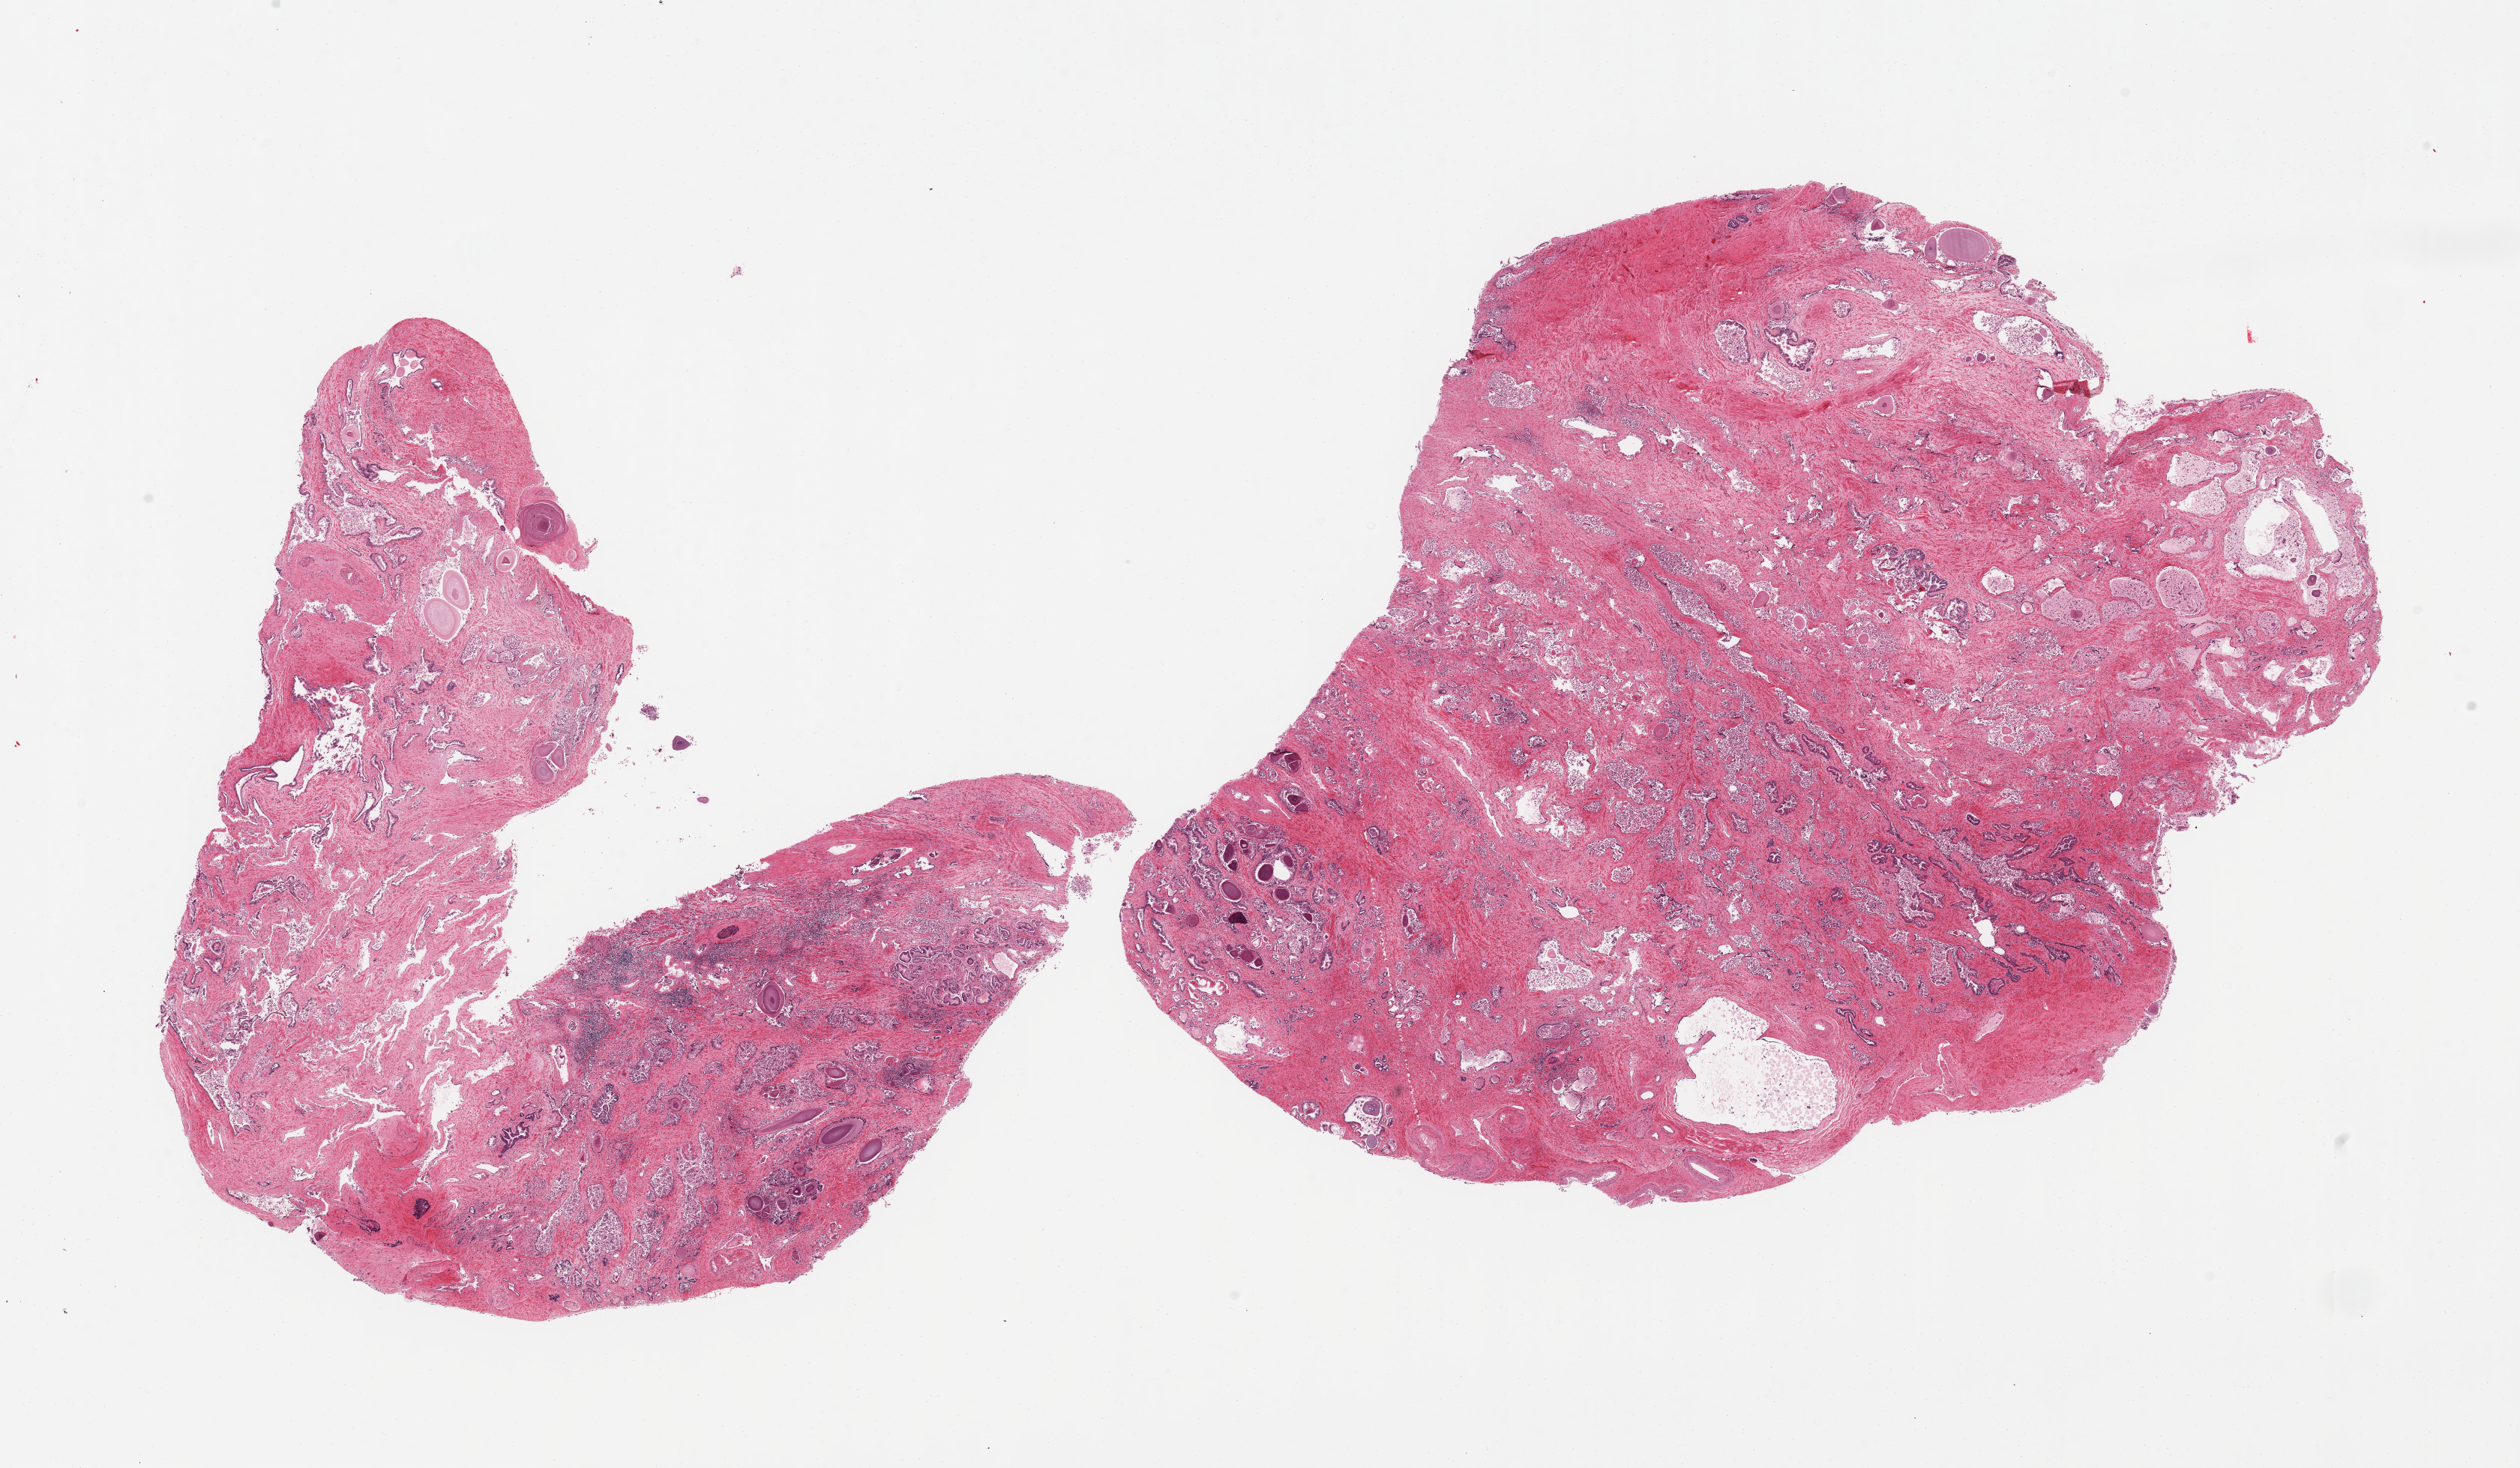
Haematoxylin and eosin whole-slide image, brightfield, low-resolution overview of the scanned area, about 26.6 x 15.5 mm (acquisition: 20x scan). PAXgene-fixed paraffin-embedded (PFPE) section. Target tissue: prostate. Tissue donor sample. Donor: male.
Reviewer comment on this tissue sample: 2 pieces, glandular elements with moderate-several autolysis.